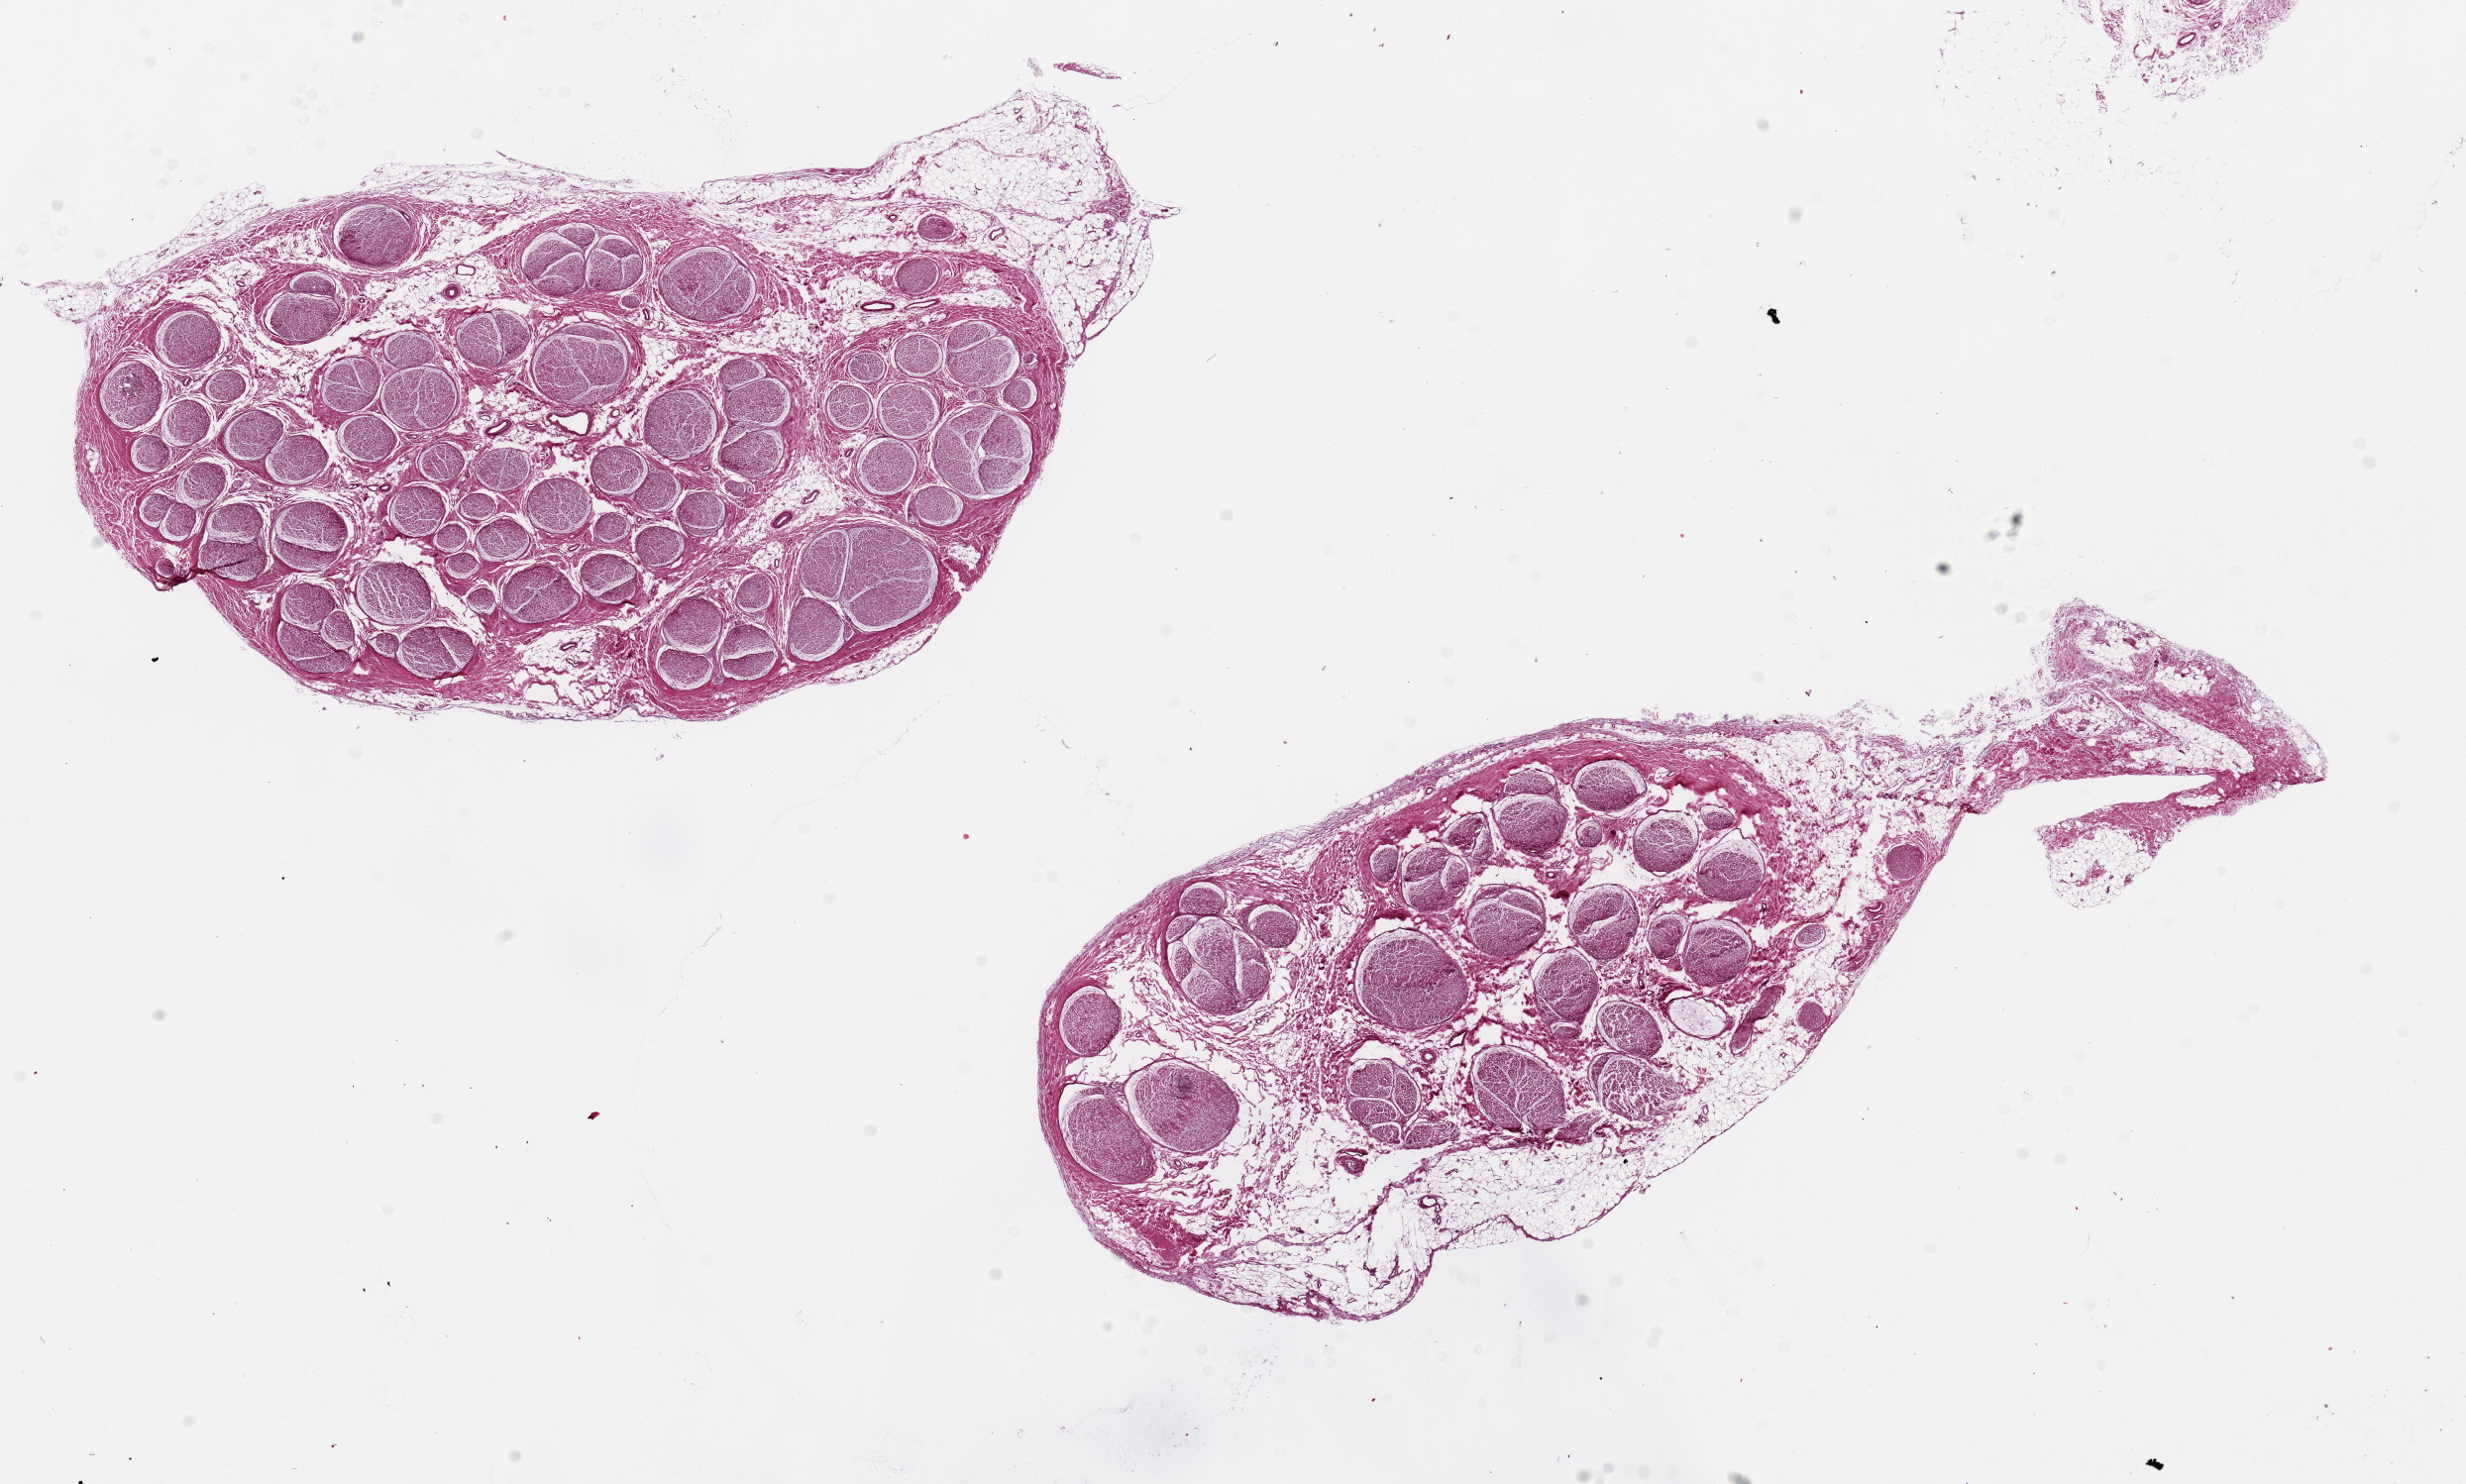
Hematoxylin and eosin (H&E) whole-slide image, shown as a low-resolution overview of the whole scanned area (about 19.7 x 11.8 mm, slide scanned at 20x); PAXgene-fixed, paraffin-embedded tissue; sampled site (target tissue): tibial nerve; tissue donor sample. Female donor.
• reviewer comment on this tissue sample: 2 pieces ~6mm d. some interstital fat and focal adherent fat, up to 1mm thick